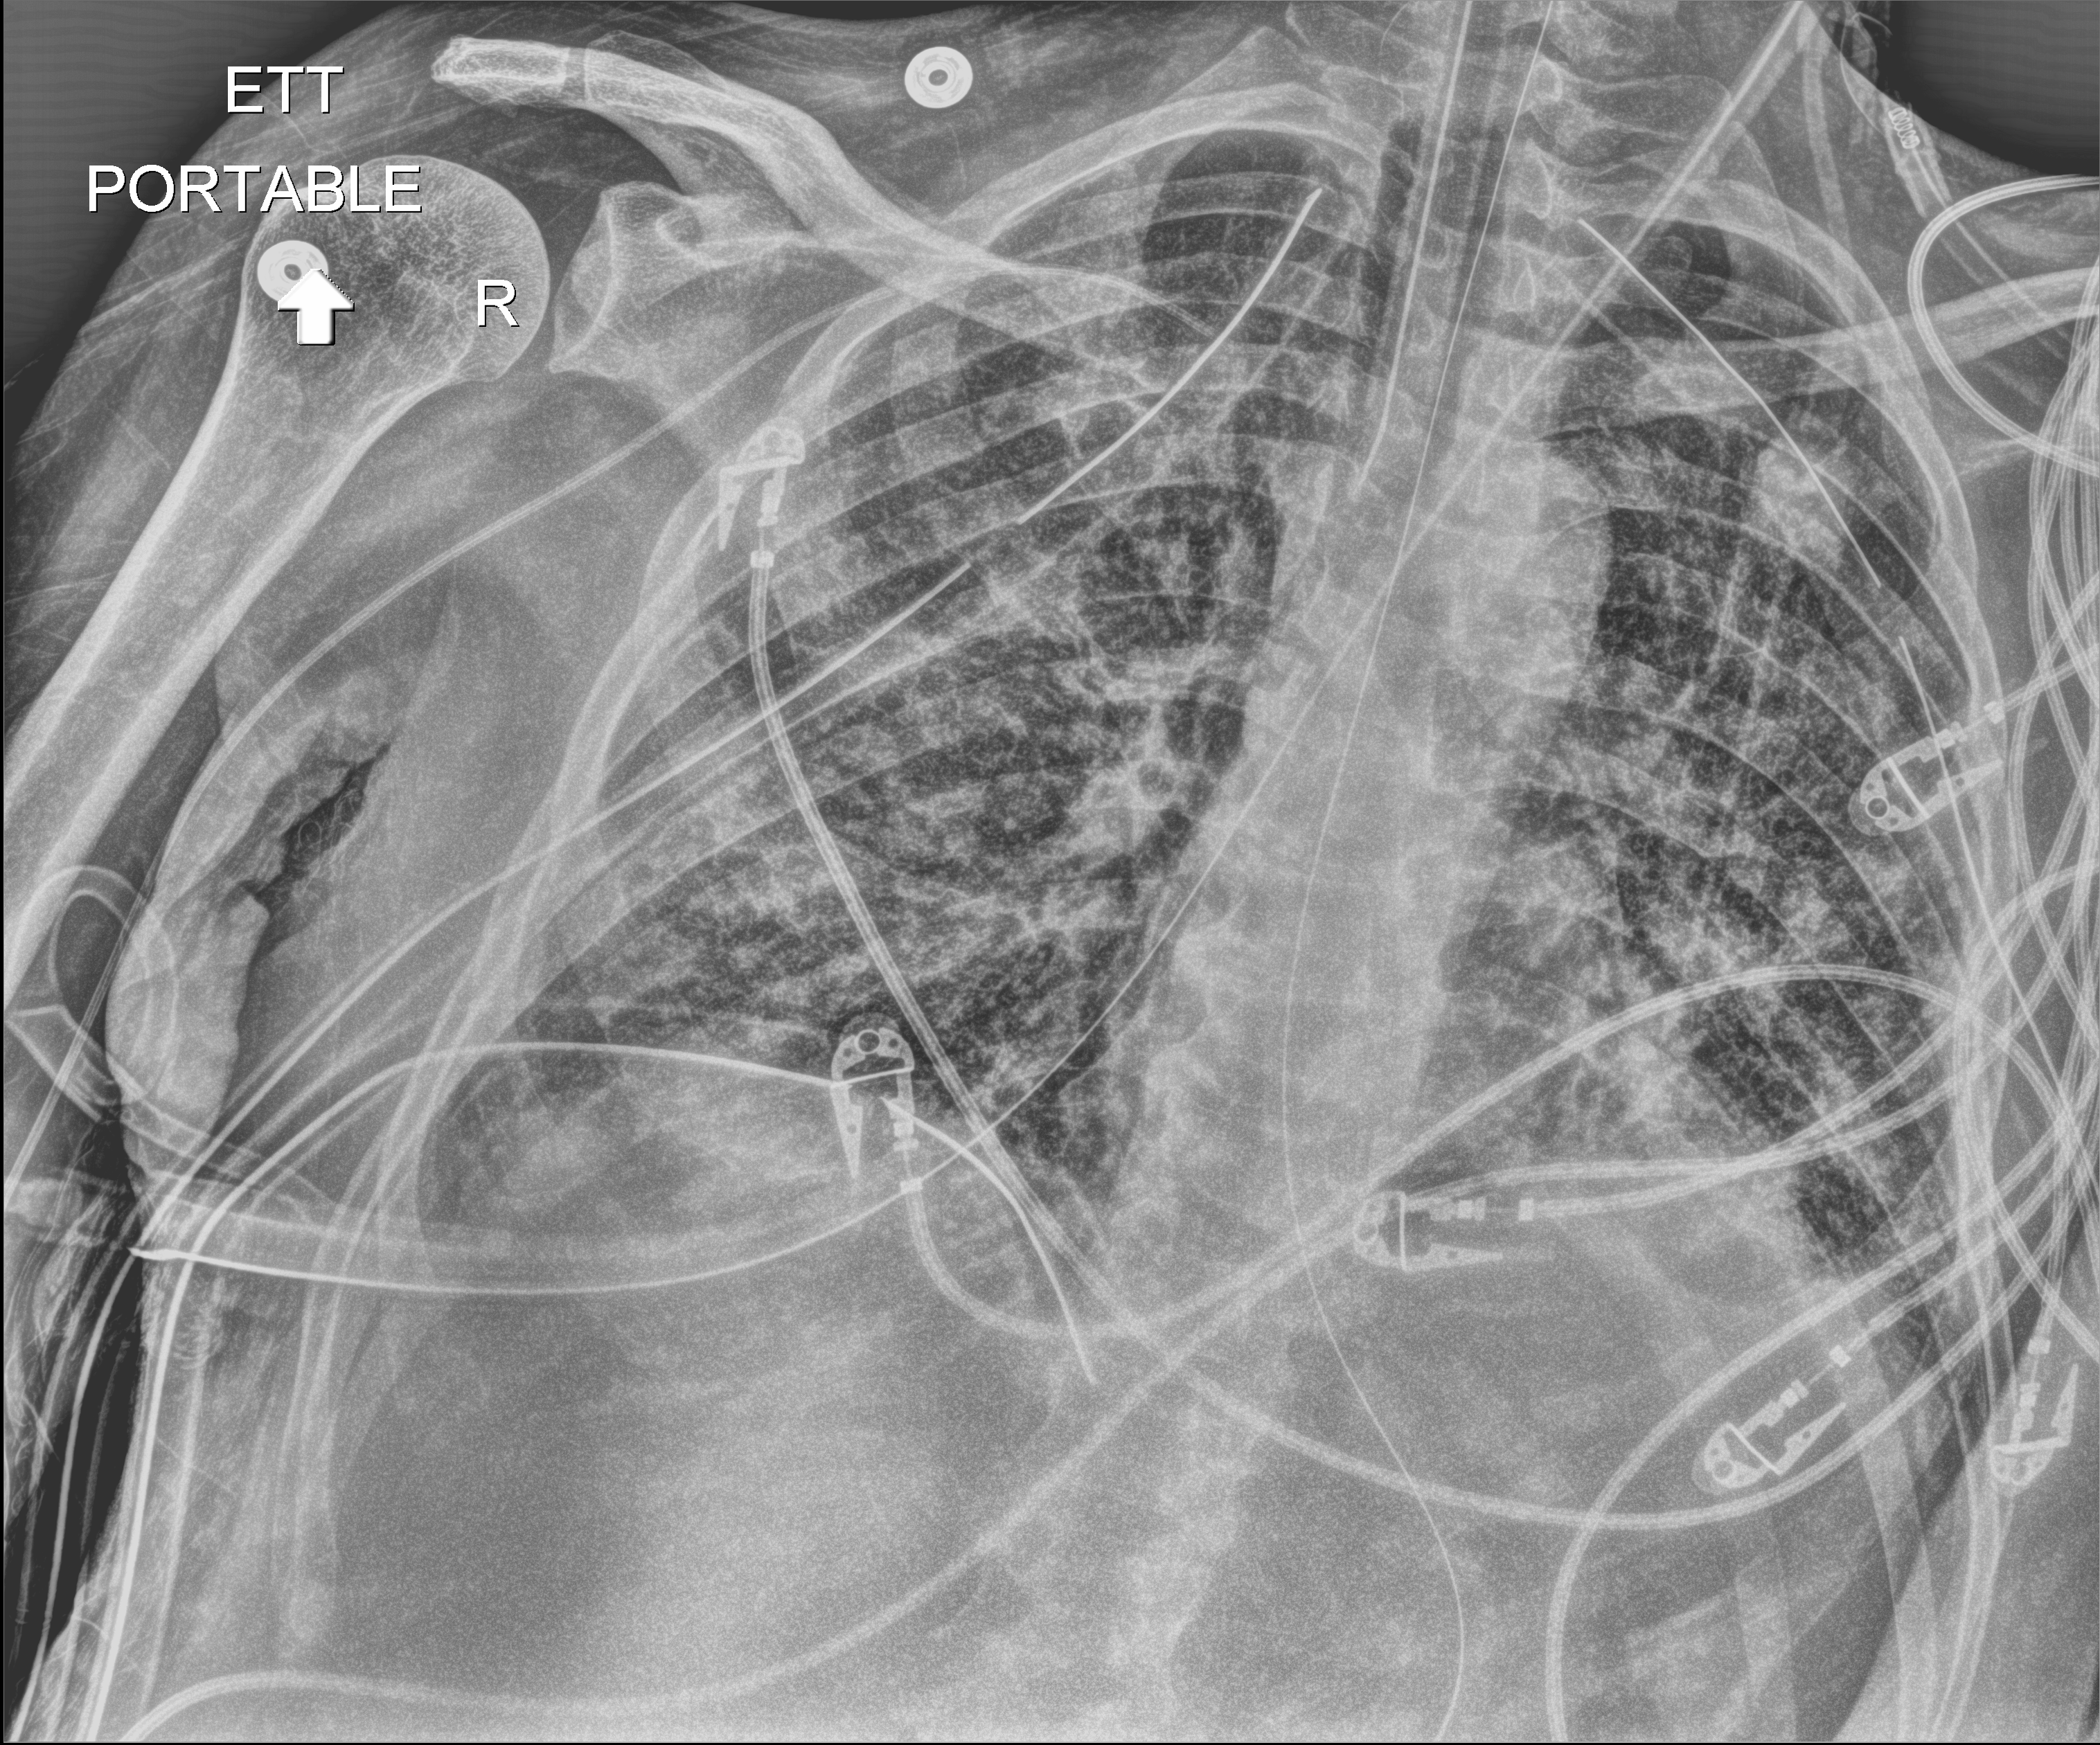
Portable chest radiograph, anteroposterior (AP) projection. Patient hospitalised with COVID-19; male, aged 18–59 years.
Hospital-stay facts (about this admission, not read from this image; timing relative to this image not recorded):
- mechanically ventilated during this hospital stay: yes